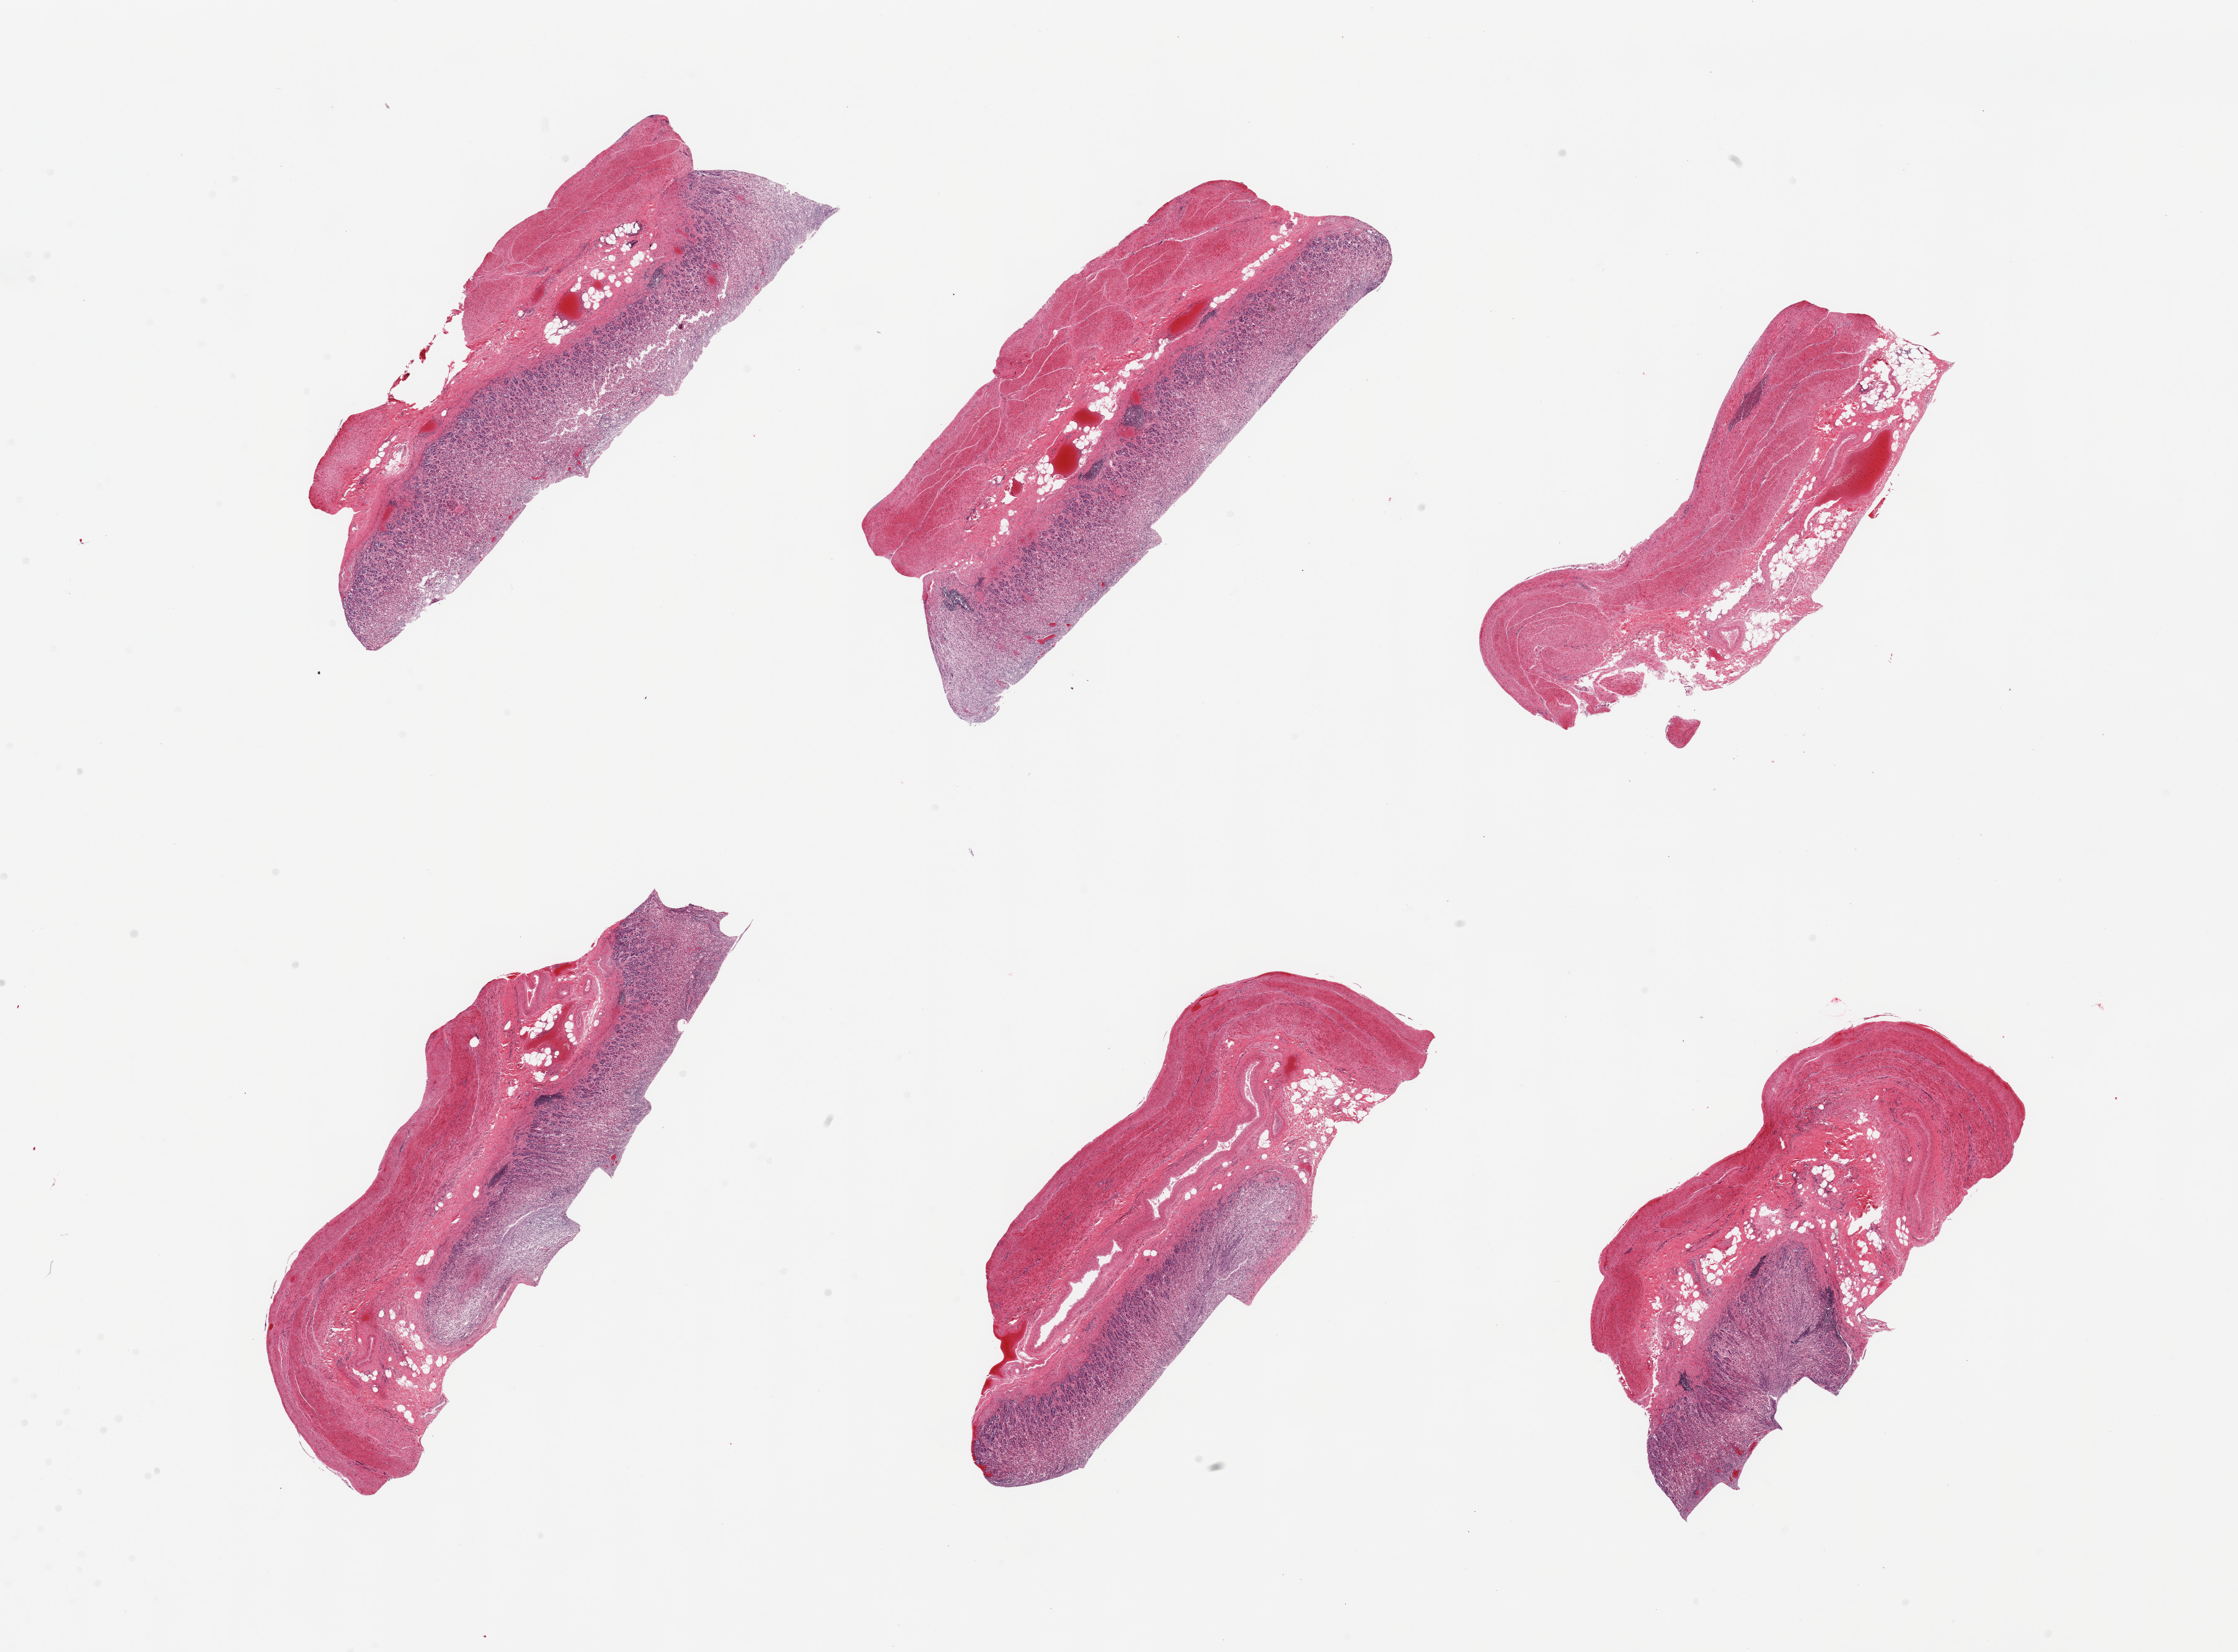
Whole-slide image, haematoxylin and eosin stain, brightfield, low-resolution overview of the scanned area, about 28.5 x 21.1 mm. Male donor.
Specimen: PAXgene-fixed, paraffin-embedded tissue; sampled site (target tissue): stomach; donor tissue sample.